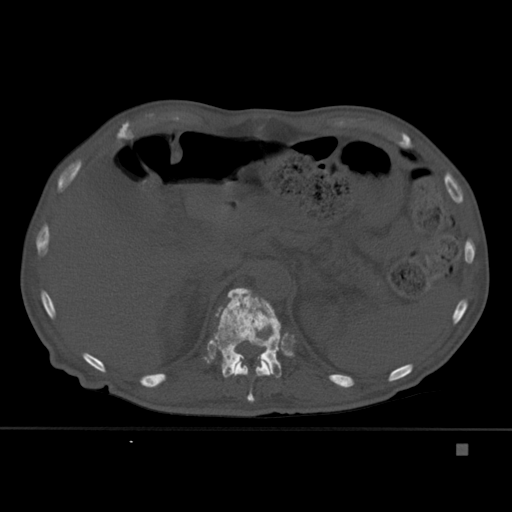
CT including the spine, one axial slice; slice 206 of 451 in the series (ordered by position); bone window (W 1800 / L 400 HU); 1.5 mm slice thickness; 512 × 512 image matrix, field of view 378 × 378 mm. Patient: male, 75 years. From the clinical record (not read from this slice): primary cancer: prostate.
Outlined on this slice (semi-automatic segmentation, software-assisted and operator-edited):
- T11 vertebra: bounding box [x1, y1, x2, y2] px = [233, 358, 272, 402]
- T12 vertebra: [210, 288, 282, 378]